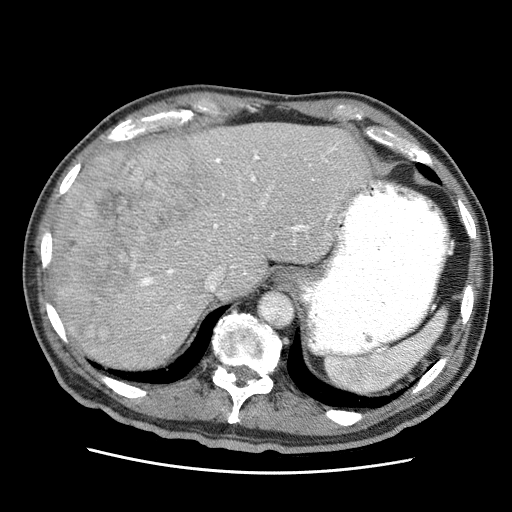
Contrast-enhanced abdominal CT (liver protocol), one axial slice. Slice 47 of 75 in the series (ordered by position). Reconstruction kernel STANDARD. 120 kVp. Soft-tissue window (W 400 / L 40 HU). 512 × 512 image matrix, field of view 360 × 360 mm. Case-level facts recorded for this patient, not image findings: diagnosis: hepatocellular carcinoma (patient treated with transarterial chemoembolisation; whether this scan precedes or follows treatment is not stated here); TNM stage (as recorded): Stage-IIIA; Child-Pugh class: A; tumour differentiation: well differentiated.
Structures marked on this image (semi-automatic segmentation, software-assisted and operator-edited):
- abdominal aorta: bounding box <260,292,293,326> (left, top, right, bottom; pixels)
- liver parenchyma outside the tumour (the mass and vessels are separate outlines, so this box may not span the whole liver): <52,122,370,368>
- mass: <53,145,216,344>
- liver vessels: <133,143,338,340>